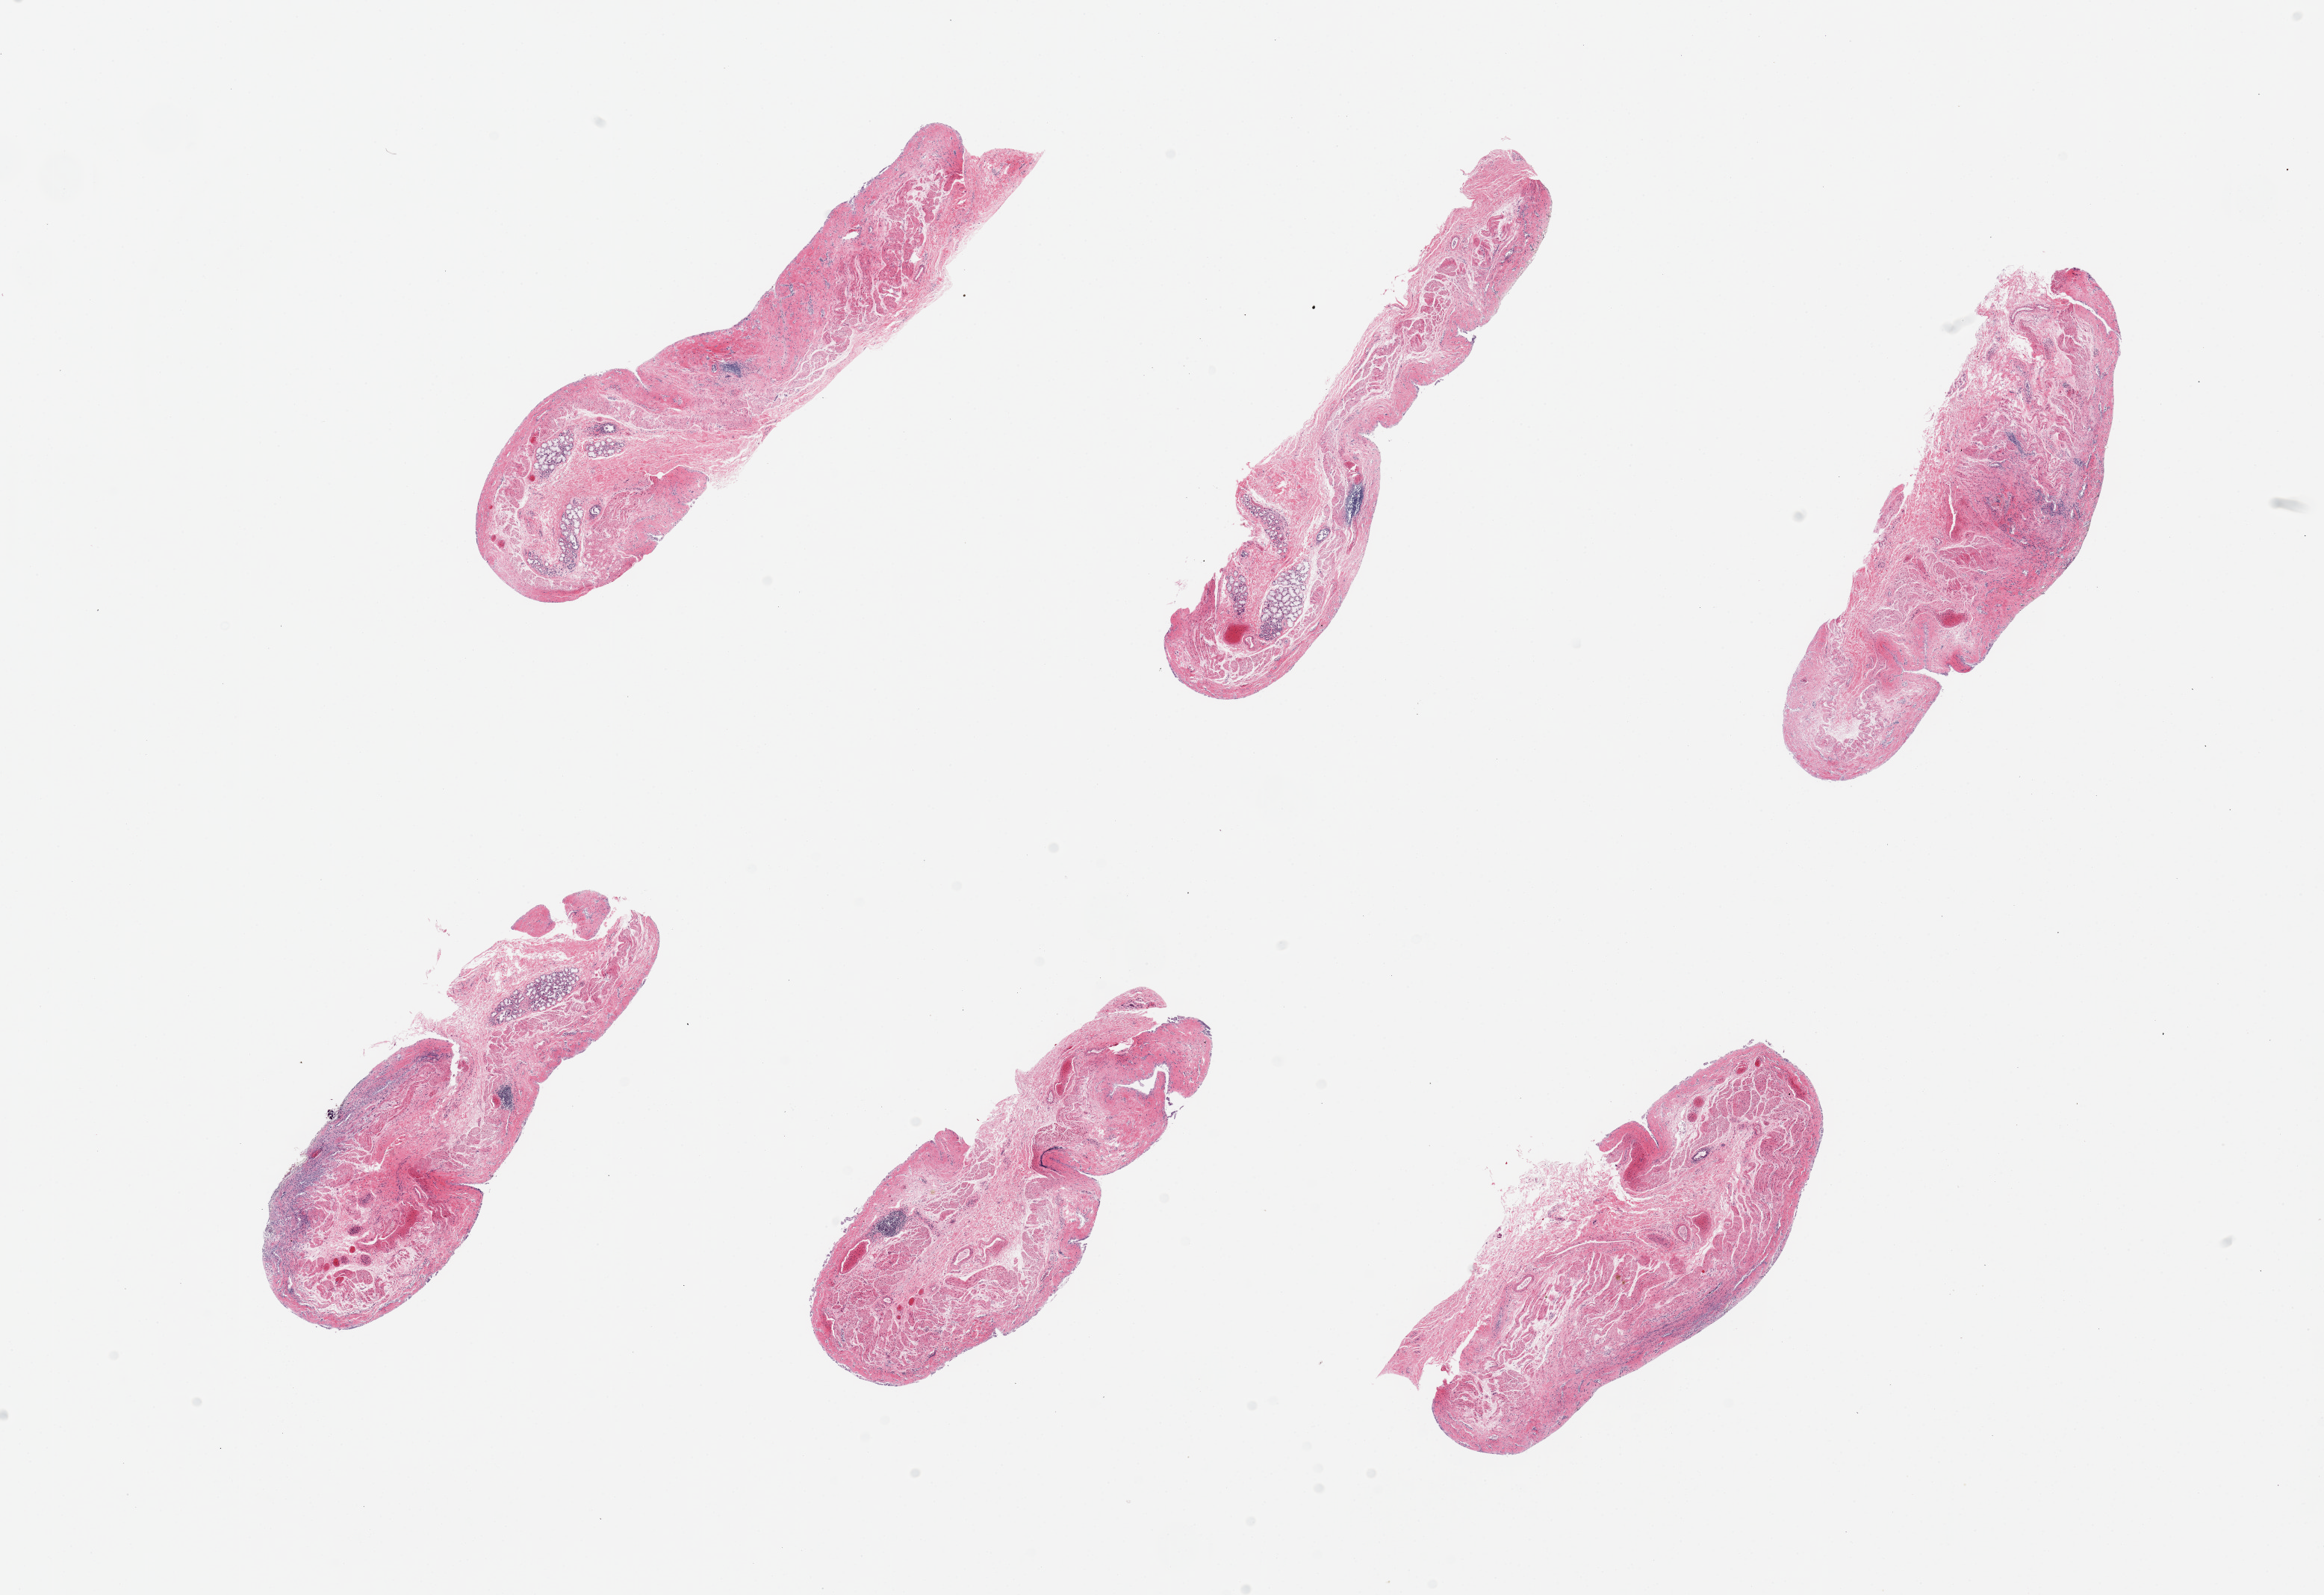
Whole-slide image, haematoxylin and eosin stain — a low-resolution overview of the entire scanned area, about 24.6 x 16.9 mm (slide scanned at 20x); PAXgene-fixed, paraffin-embedded tissue; section of esophageal mucous membrane (target tissue); tissue donor sample.
• review note (as recorded): 6 pieces, unusually advanced autolysis; squamous mucosa totally sloughed; Residual submucosal mucus glands present but poorly preserved